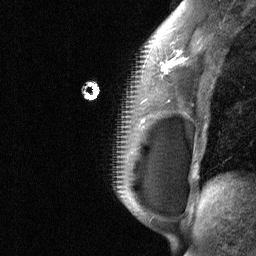
Breast MRI (dynamic contrast-enhanced), one sagittal slice. Position 44 of 64 along the scan axis. Dynamic contrast-enhanced study with each time point stored as its own series, time point 2 of 3 at this slice position (early post-contrast, ordered by acquisition time). 1.5 T. TE 4.8 ms, TR 27 ms. 256 × 256 image matrix, field of view 200 × 200 mm. Patient: female, 34 years. From the clinical record (not read from this slice): setting: breast cancer imaged before/during neoadjuvant chemotherapy; receptor status: HR-positive, HER2-negative.
Outlined on this slice (semi-automatically segmented with operator editing):
- analysis volume of interest (the breast-tissue region the enhancement analysis was run in; not a lesion): bounding box [x1, y1, x2, y2] px = [92, 50, 188, 185]
- tumour enhancement mask (voxels above the 90 % enhancement threshold inside the analysis volume of interest): [161, 53, 184, 73]